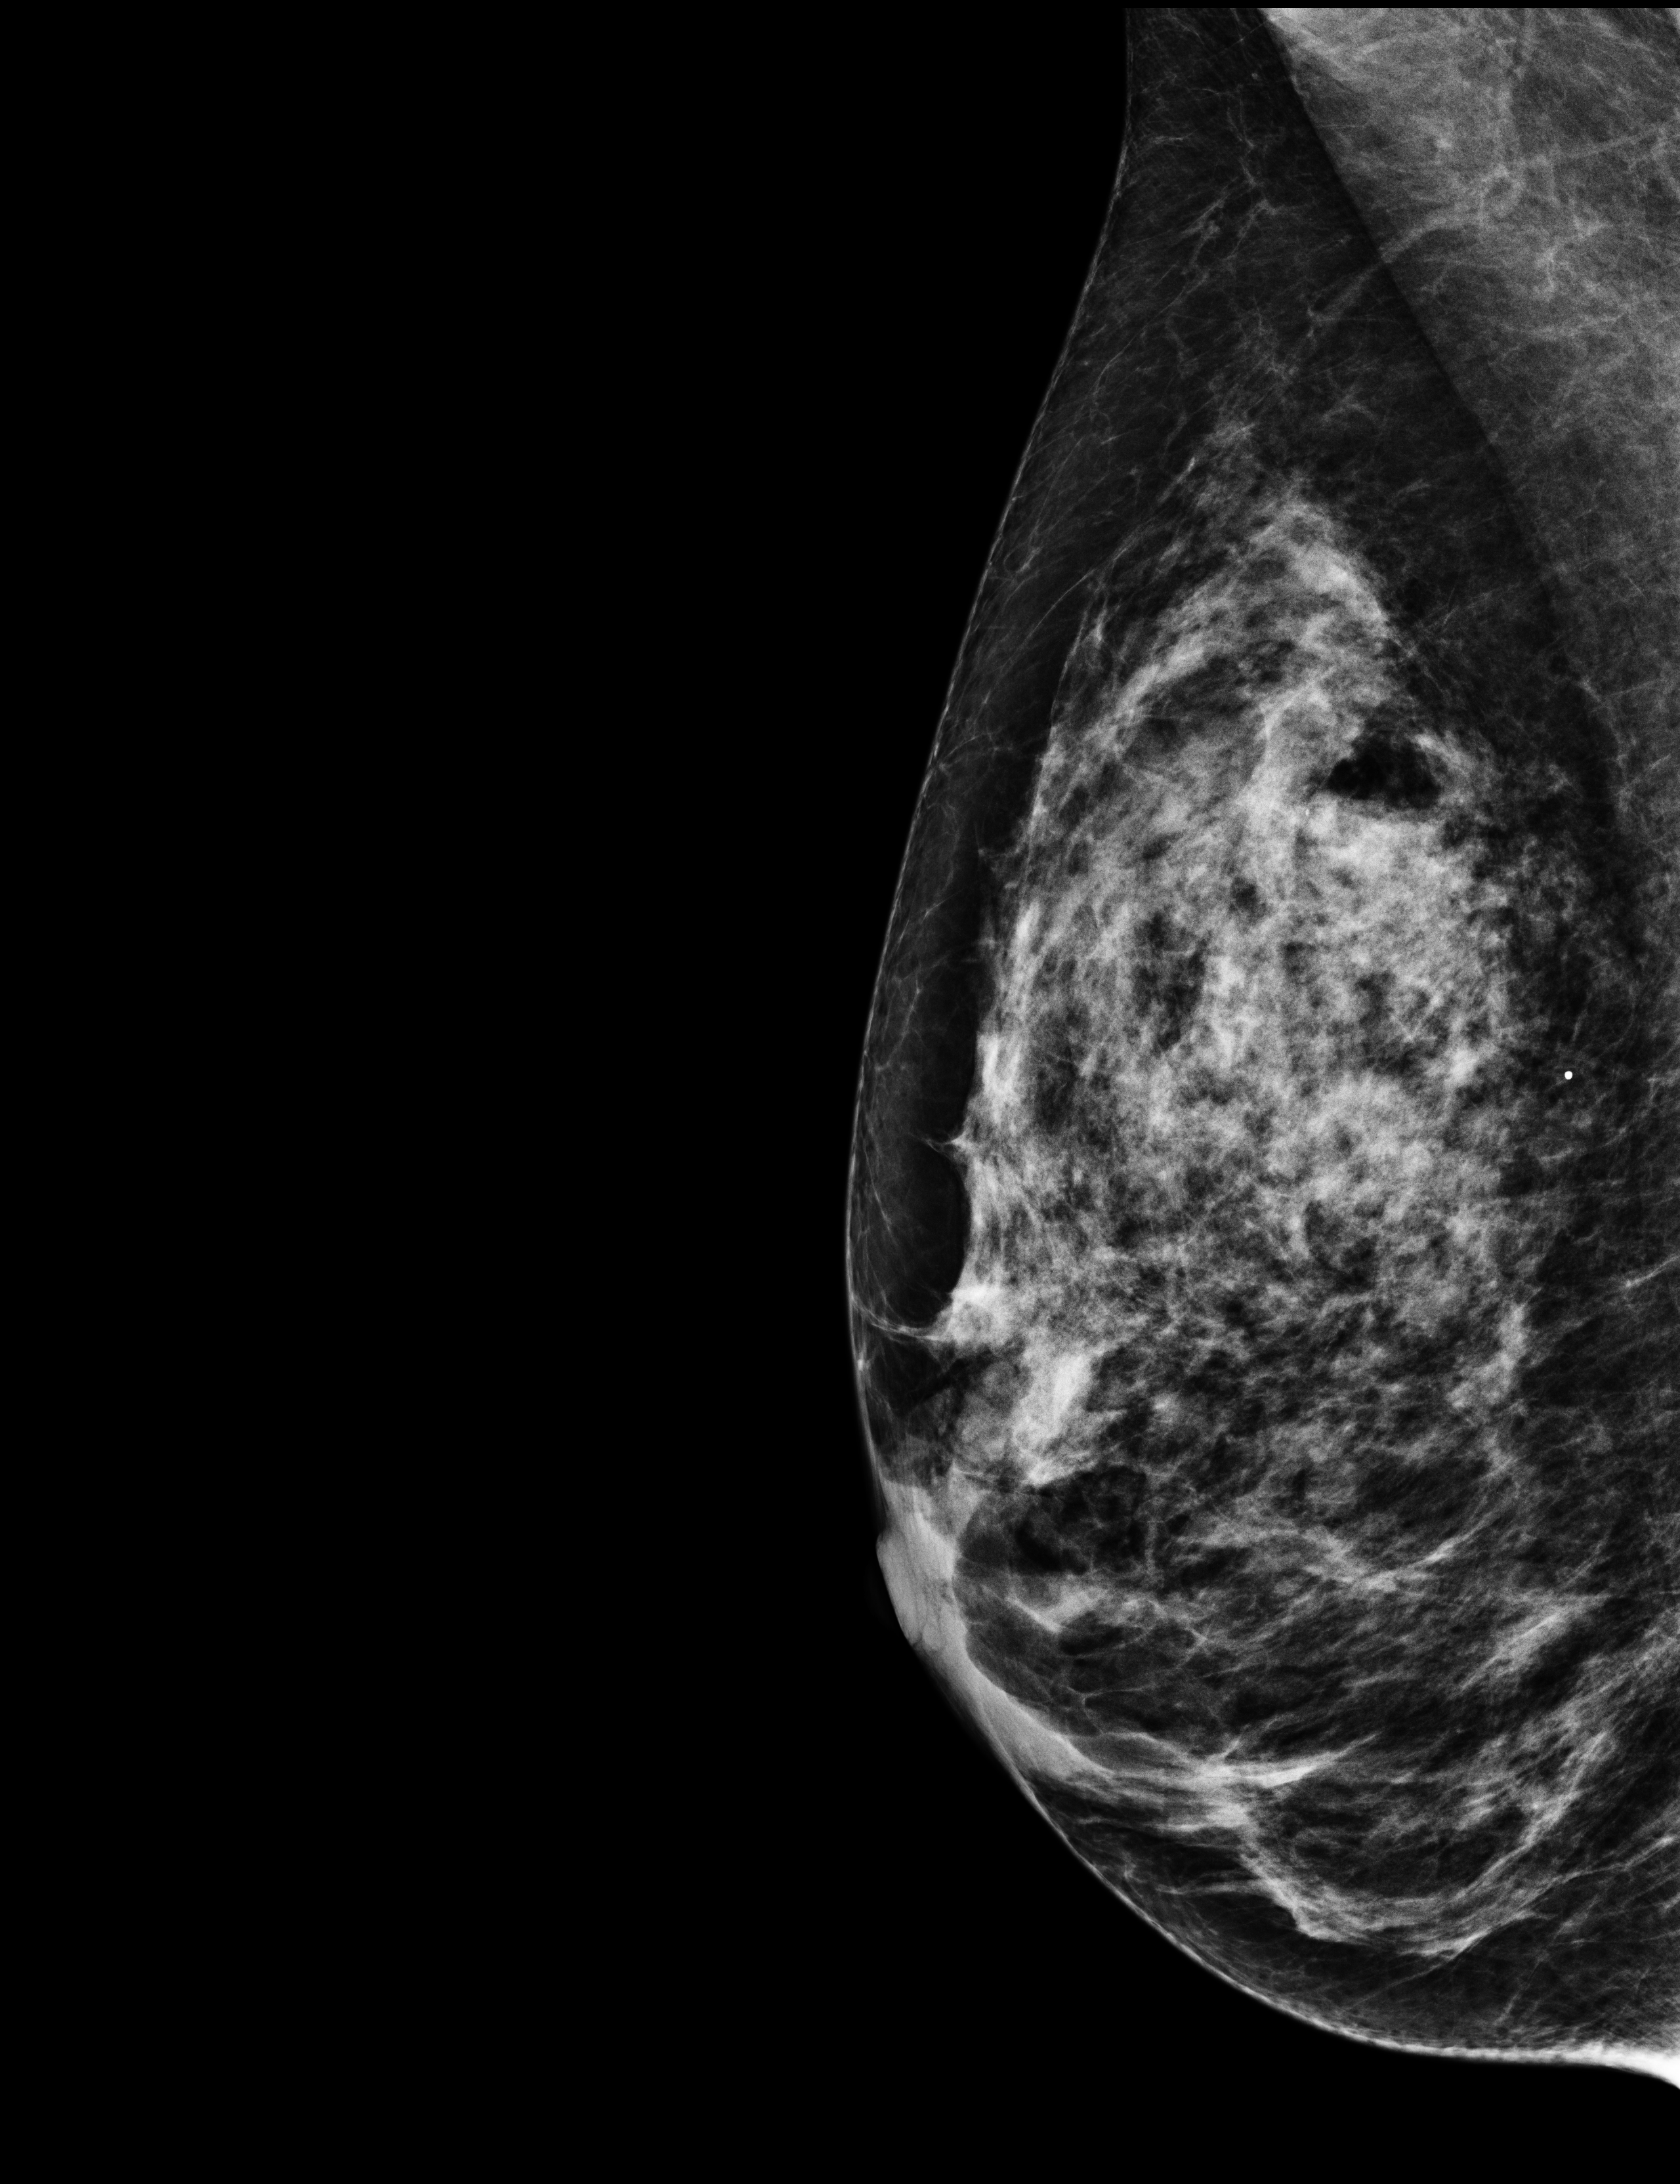
Full-field digital mammogram (FFDM); right breast; medio-lateral oblique projection; annual screening mammography examination; compressed breast thickness 48 mm; system: Selenia Dimensions. Patient aged 59 years (female).
- breast density at the screening exam (both breasts): heterogeneously dense (BI-RADS density category c)
- final BI-RADS assessment for this screening round (tomosynthesis exam, both breasts): category 1
- recall: no recall after this screen